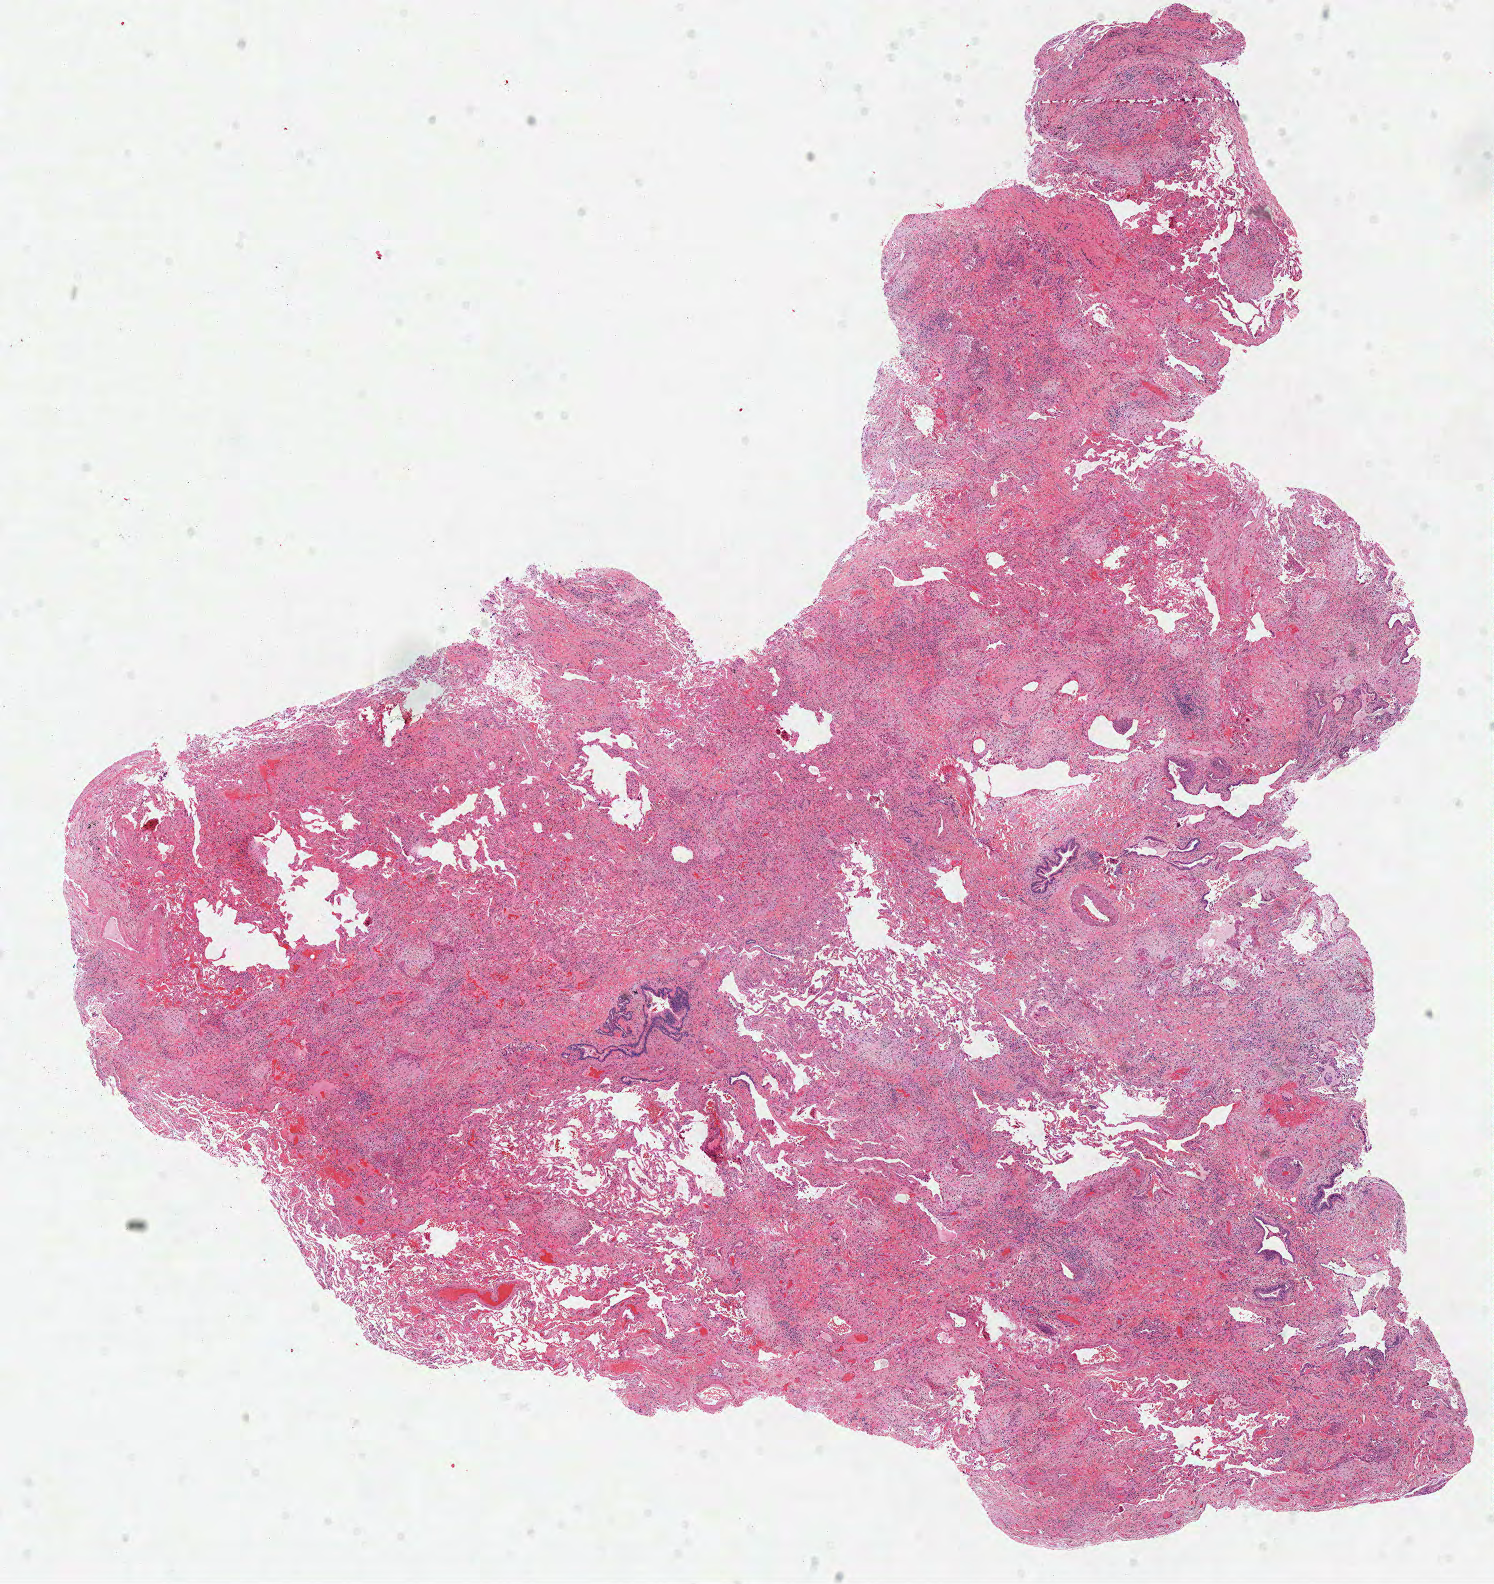
Hematoxylin and eosin (H&E) stained whole-slide image, whole scanned area (about 11.7 x 12.5 mm, slide scanned at 40x) shown as a low-resolution overview; frozen section from the top of the tissue portion; solid tissue normal (non-tumour tissue) sample from the lung. Patient: male, age at initial diagnosis 76 years.
This section: solid tissue normal sample (biorepository sample class). Patient diagnosis: Squamous cell carcinoma, NOS (middle lobe, lung).